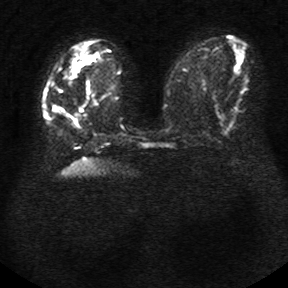
Breast MRI, one axial slice; position 12 of 34 along the scan axis; diffusion-weighted series; image 2 of 4 stored at this slice position (different b-values; order by instance number); 1.5 T; 5 mm slice thickness; 288 × 288 image matrix, field of view 340 × 340 mm. Female patient.
Annotated regions visible in this slice (outlined manually by an expert reader):
- tumour on diffusion-weighted imaging: box from (x=70, y=52) to (x=97, y=75) px